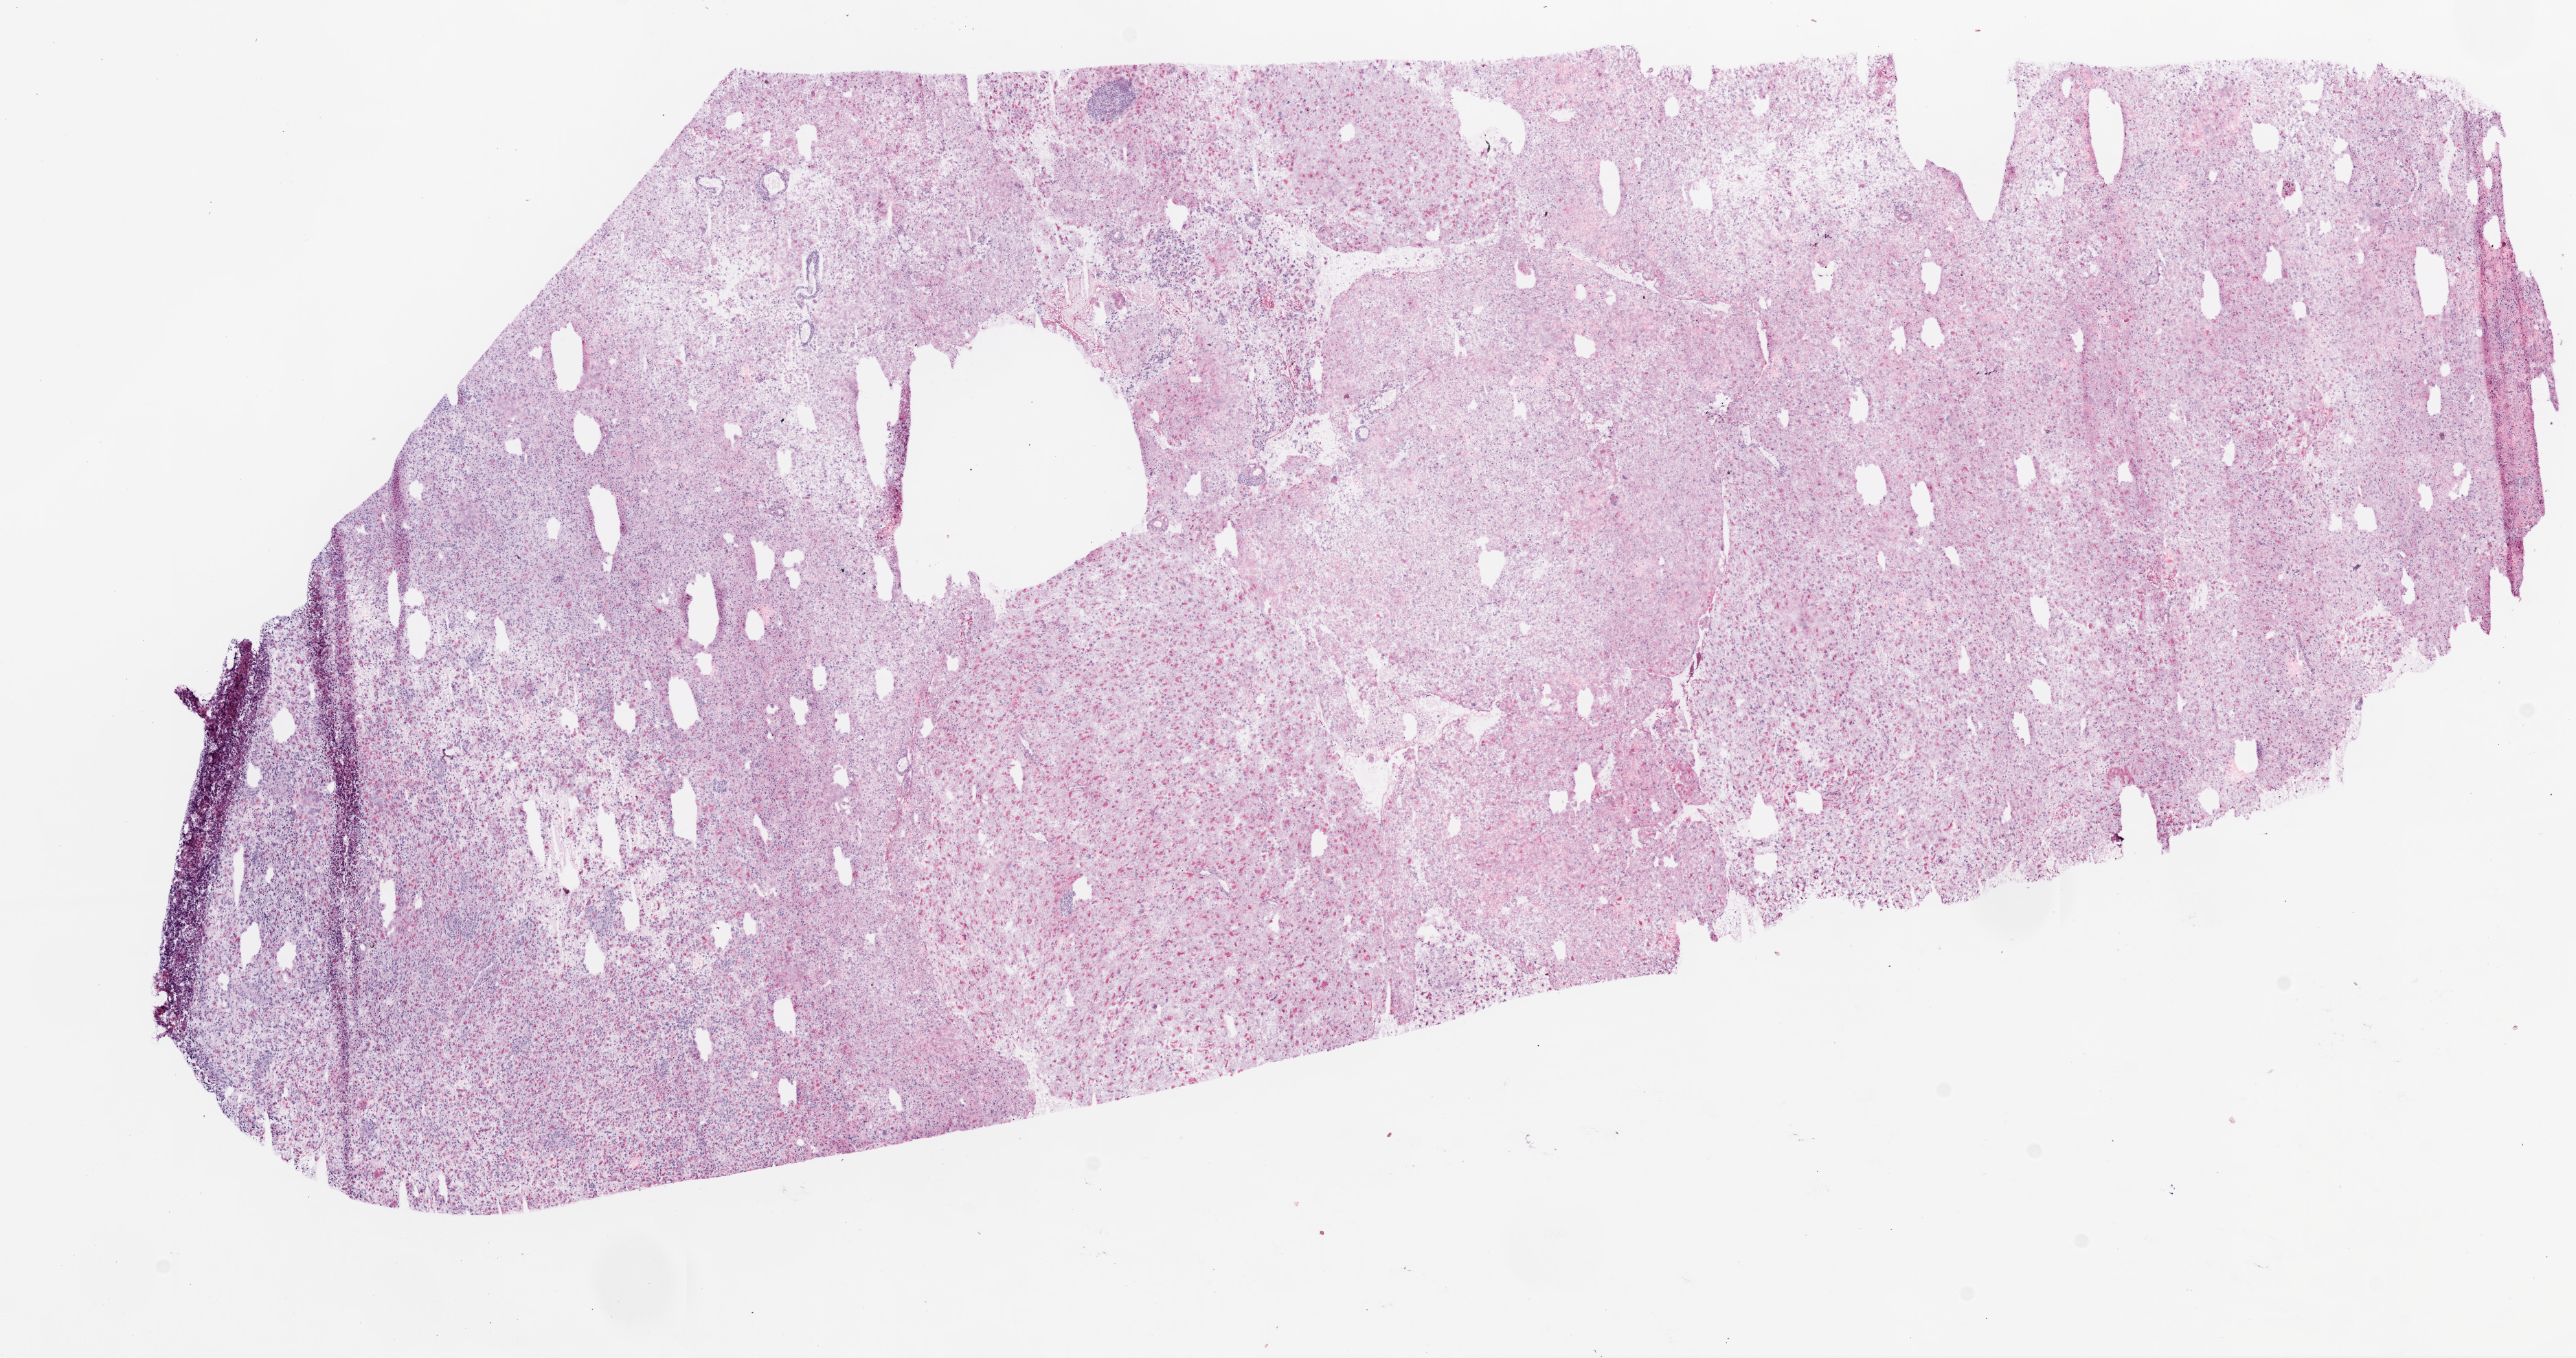
Digitized H&E tissue section (whole slide) — low-resolution overview of the scanned area, about 15.0 x 7.9 mm. Frozen section from the top of the tissue portion. Brain, primary tumour sample. Male patient; age at initial diagnosis 76 years. Composition of this section per pathologist review: tumour cells 100%, tumour nuclei 80%, normal cells 0%, stromal cells 0%, necrosis 0%.
- histologic diagnosis: Glioblastoma